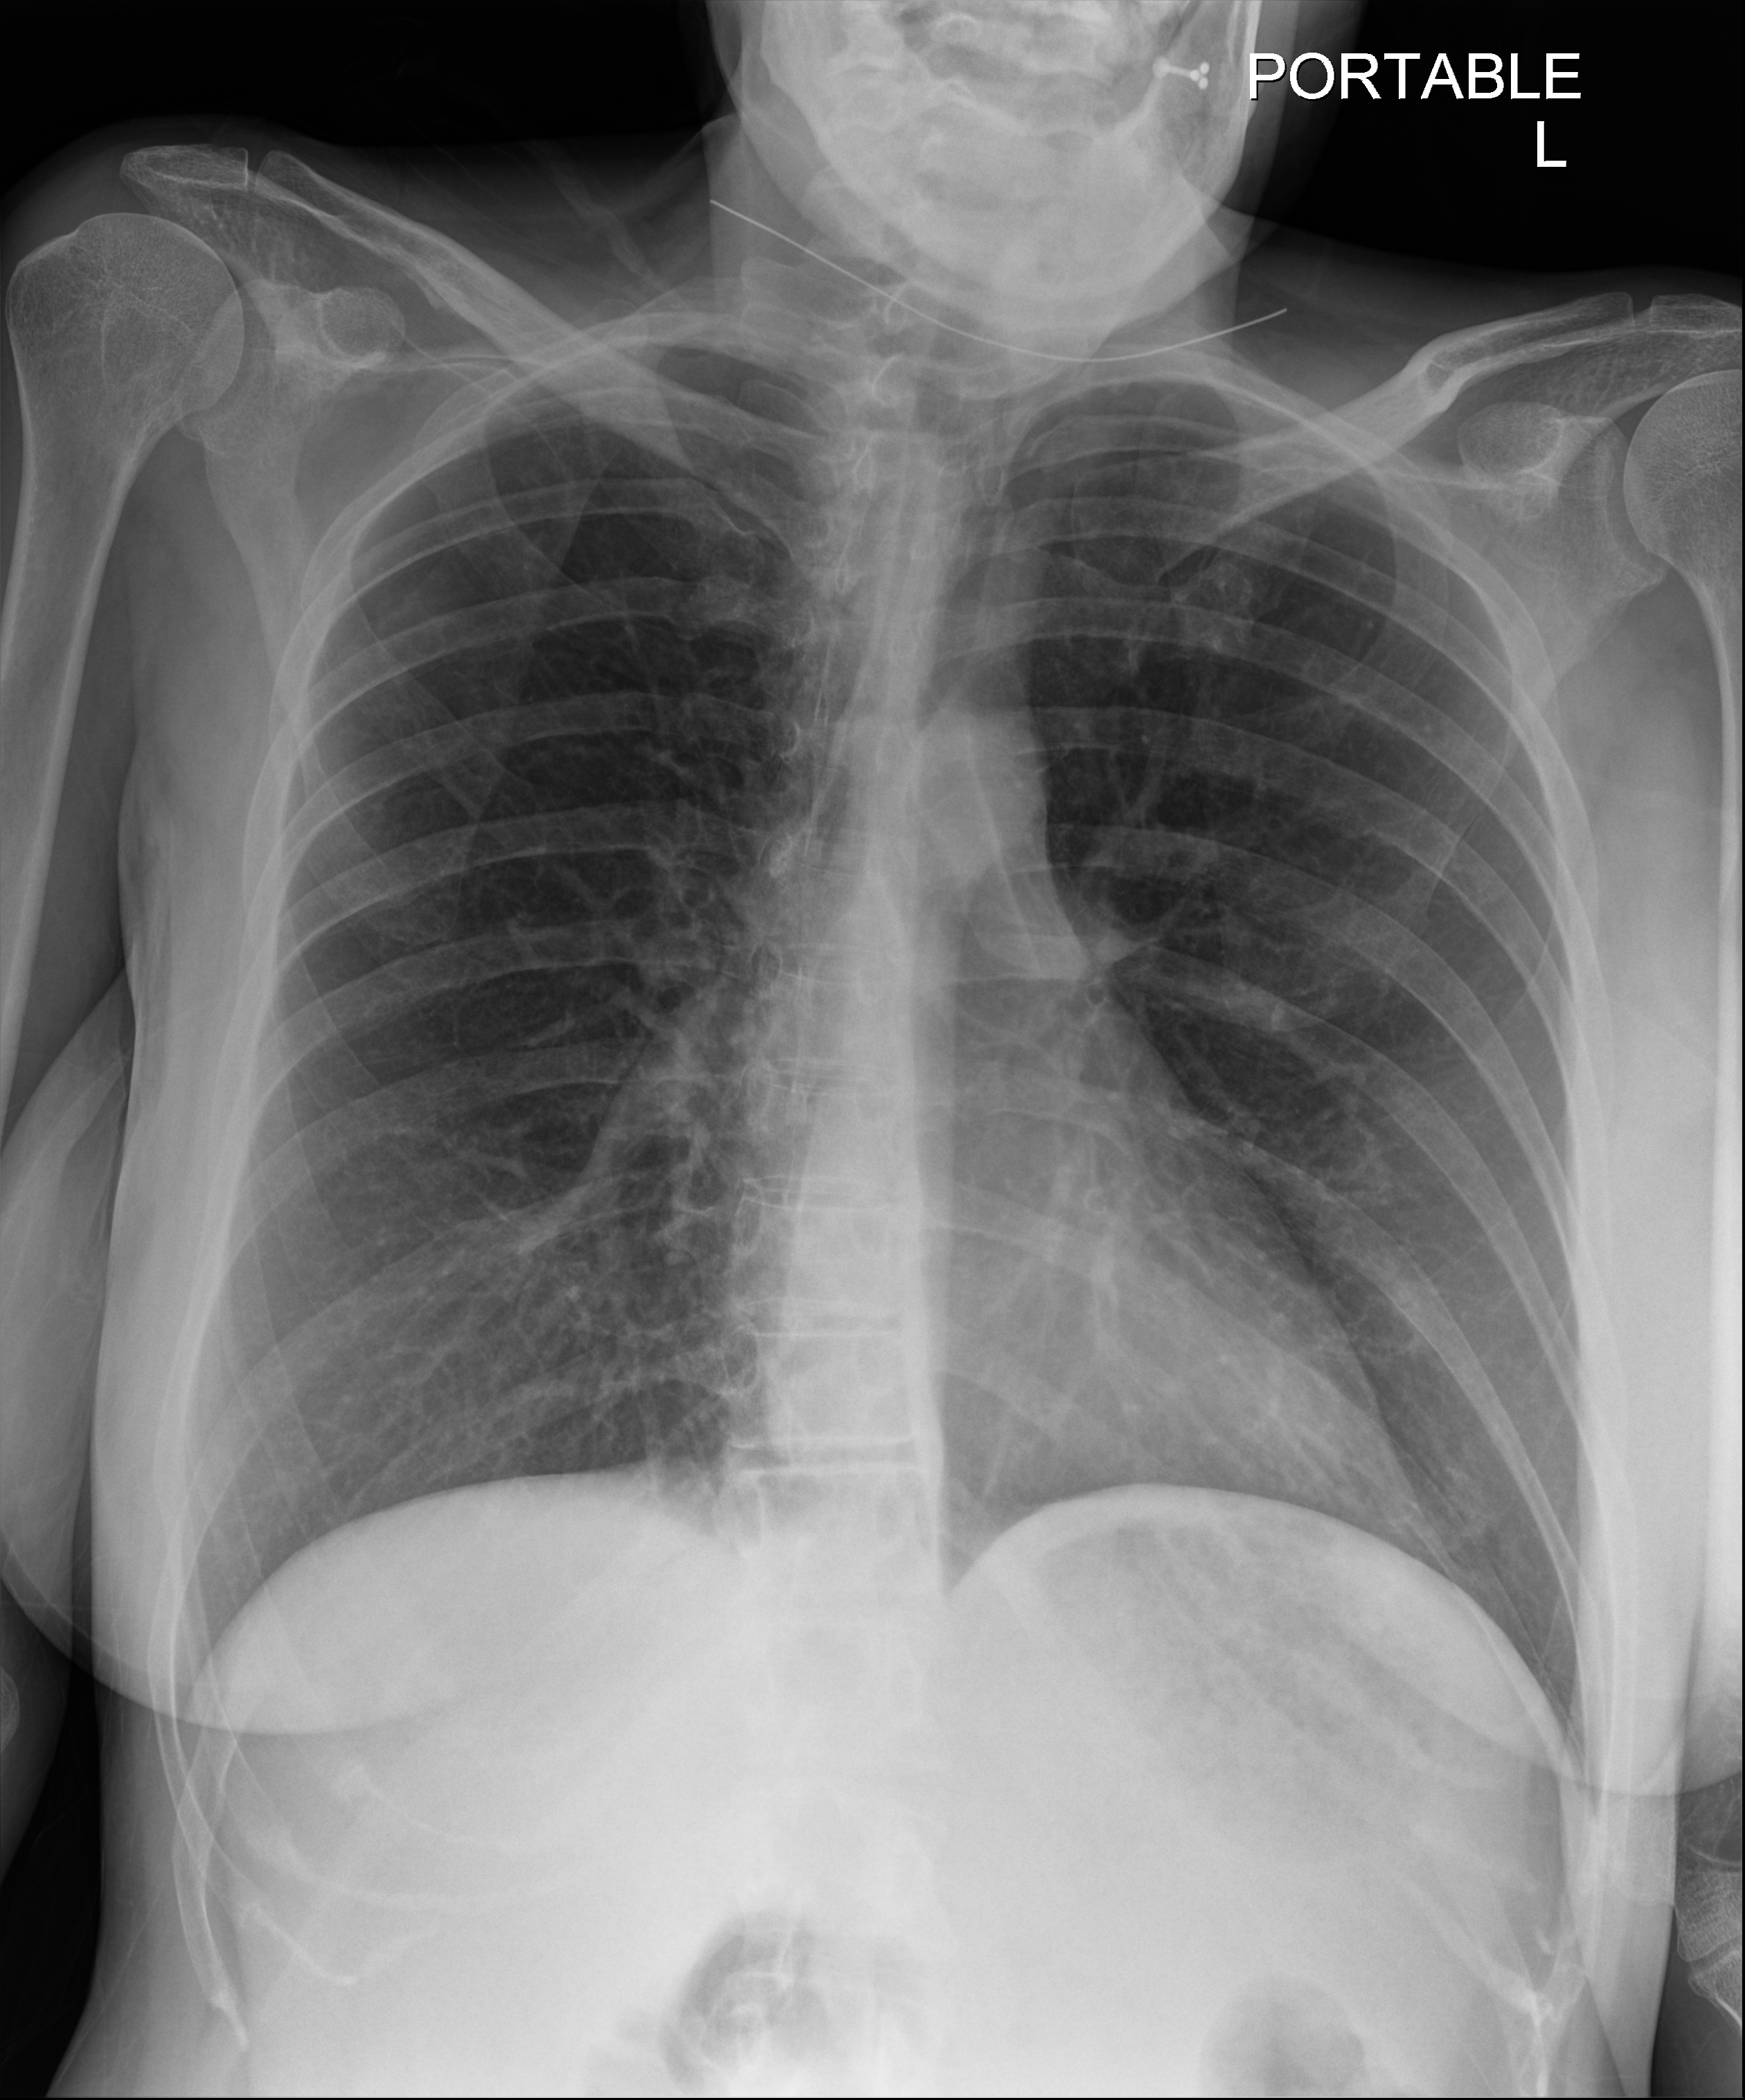
Chest X-ray. Female patient hospitalised with COVID-19, age 18–59 years.
From the hospital-stay record, not from the radiograph (when in the stay this image was taken is not recorded):
- mechanically ventilated during this hospital stay: no